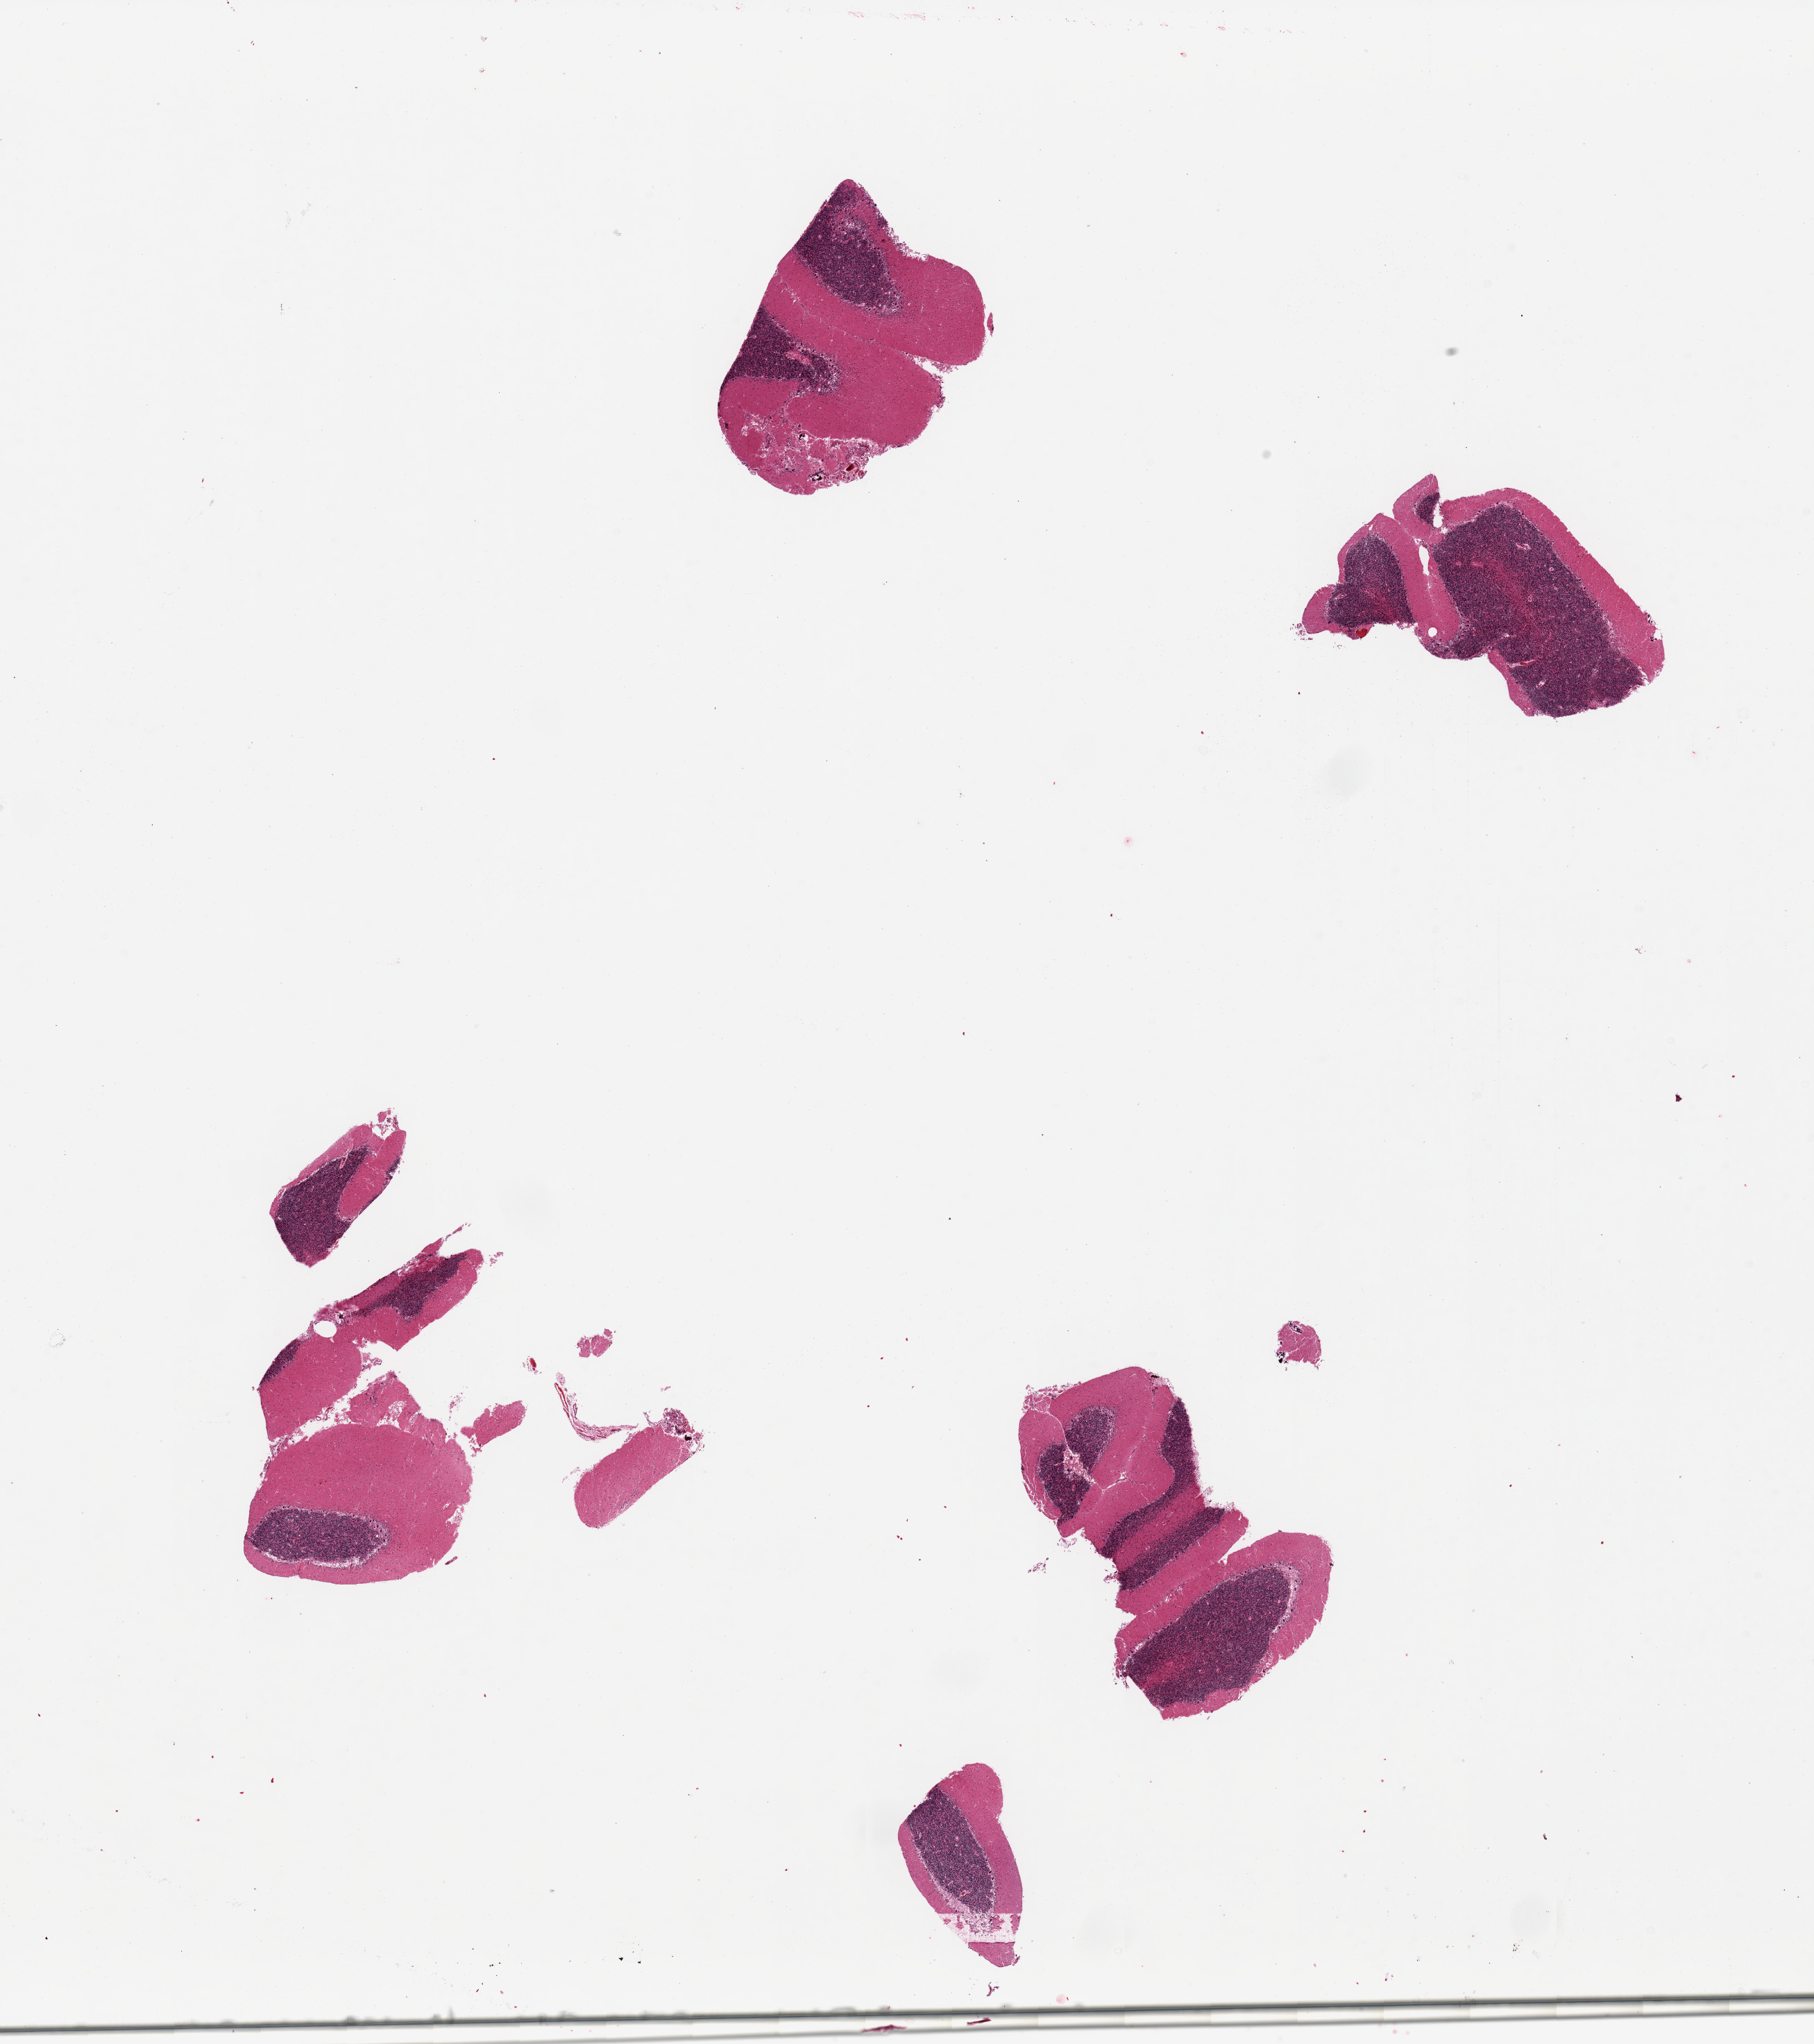
Hematoxylin and eosin (H&E) whole-slide image — low-resolution overview of the scanned area, about 20.7 x 23.3 mm (slide scanned at 20x). PAXgene-fixed, paraffin-embedded tissue. Target tissue: cerebellum. Donor tissue sample. Donor: male.
Reviewer comment on this tissue sample: 4 pieces, no abnormalities.